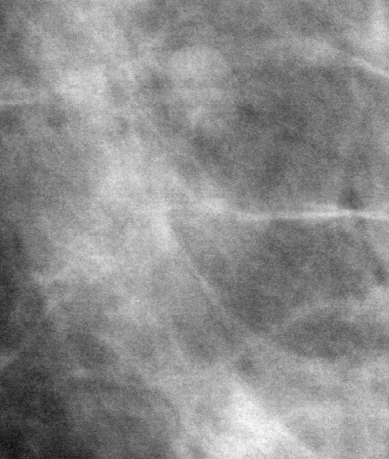
Cropped region of a digitized screen-film mammogram centred on a radiologist-marked abnormality; left breast; MLO view; BI-RADS breast density category 2 (scale 1–4).
Marked abnormality: mass, shape asymmetric breast tissue; BI-RADS assessment category 3; subtlety rating 3 on a 1 (subtle) to 5 (obvious) scale; benign without callback (not worked up further).